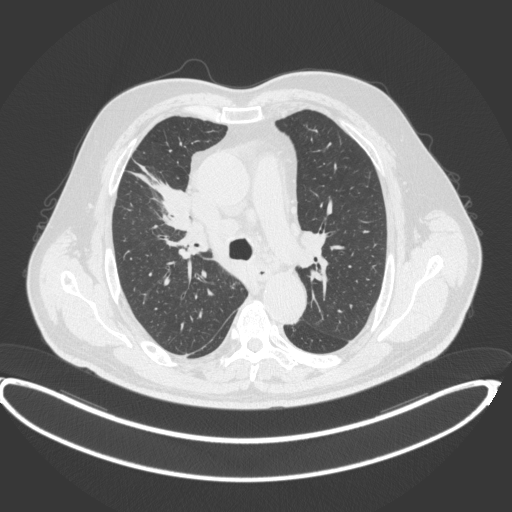
Chest CT, one axial slice. Position 274 of 395 along the scan axis. Lung window (W 1500 / L -600 HU). 1 mm slice thickness. 512 × 512 image matrix, field of view 448 × 448 mm. Male patient, age 62 years. Case-level facts recorded for this patient, not image findings: clinical TNM (as recorded): T1c N3 M1c.
Structures marked on this image (rectangle marked by the reading radiologist):
- lung tumour (recorded histology: adenocarcinoma): bounding box [x1, y1, x2, y2] px = [127, 161, 194, 230]